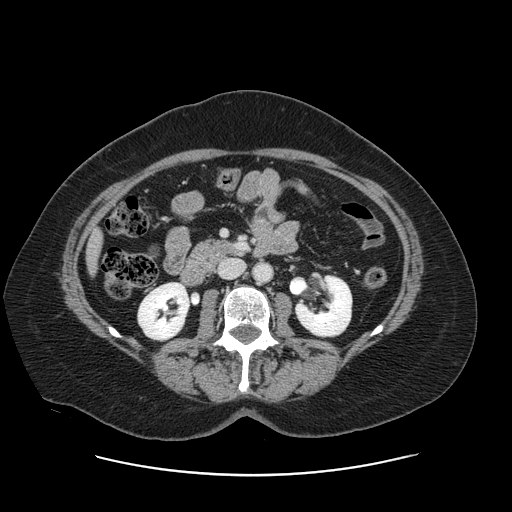
Contrast-enhanced abdominal CT, one axial slice; position 42 of 161 along the scan axis; intravenous contrast given; soft-tissue window (W 400 / L 40 HU); 2.5 mm slice thickness; 512 × 512 image matrix, field of view 398 × 398 mm. Female patient, age 62 years. Case-level facts recorded for this patient, not image findings: diagnosis: colorectal cancer liver metastases, imaged before liver resection; multiple liver metastases: no; largest metastasis: 2.5 cm; disease in both lobes: no.
Structures marked on this image (expert manual segmentation):
- liver: bounding box (x1, y1, x2, y2) in pixels: (89, 236, 100, 268)